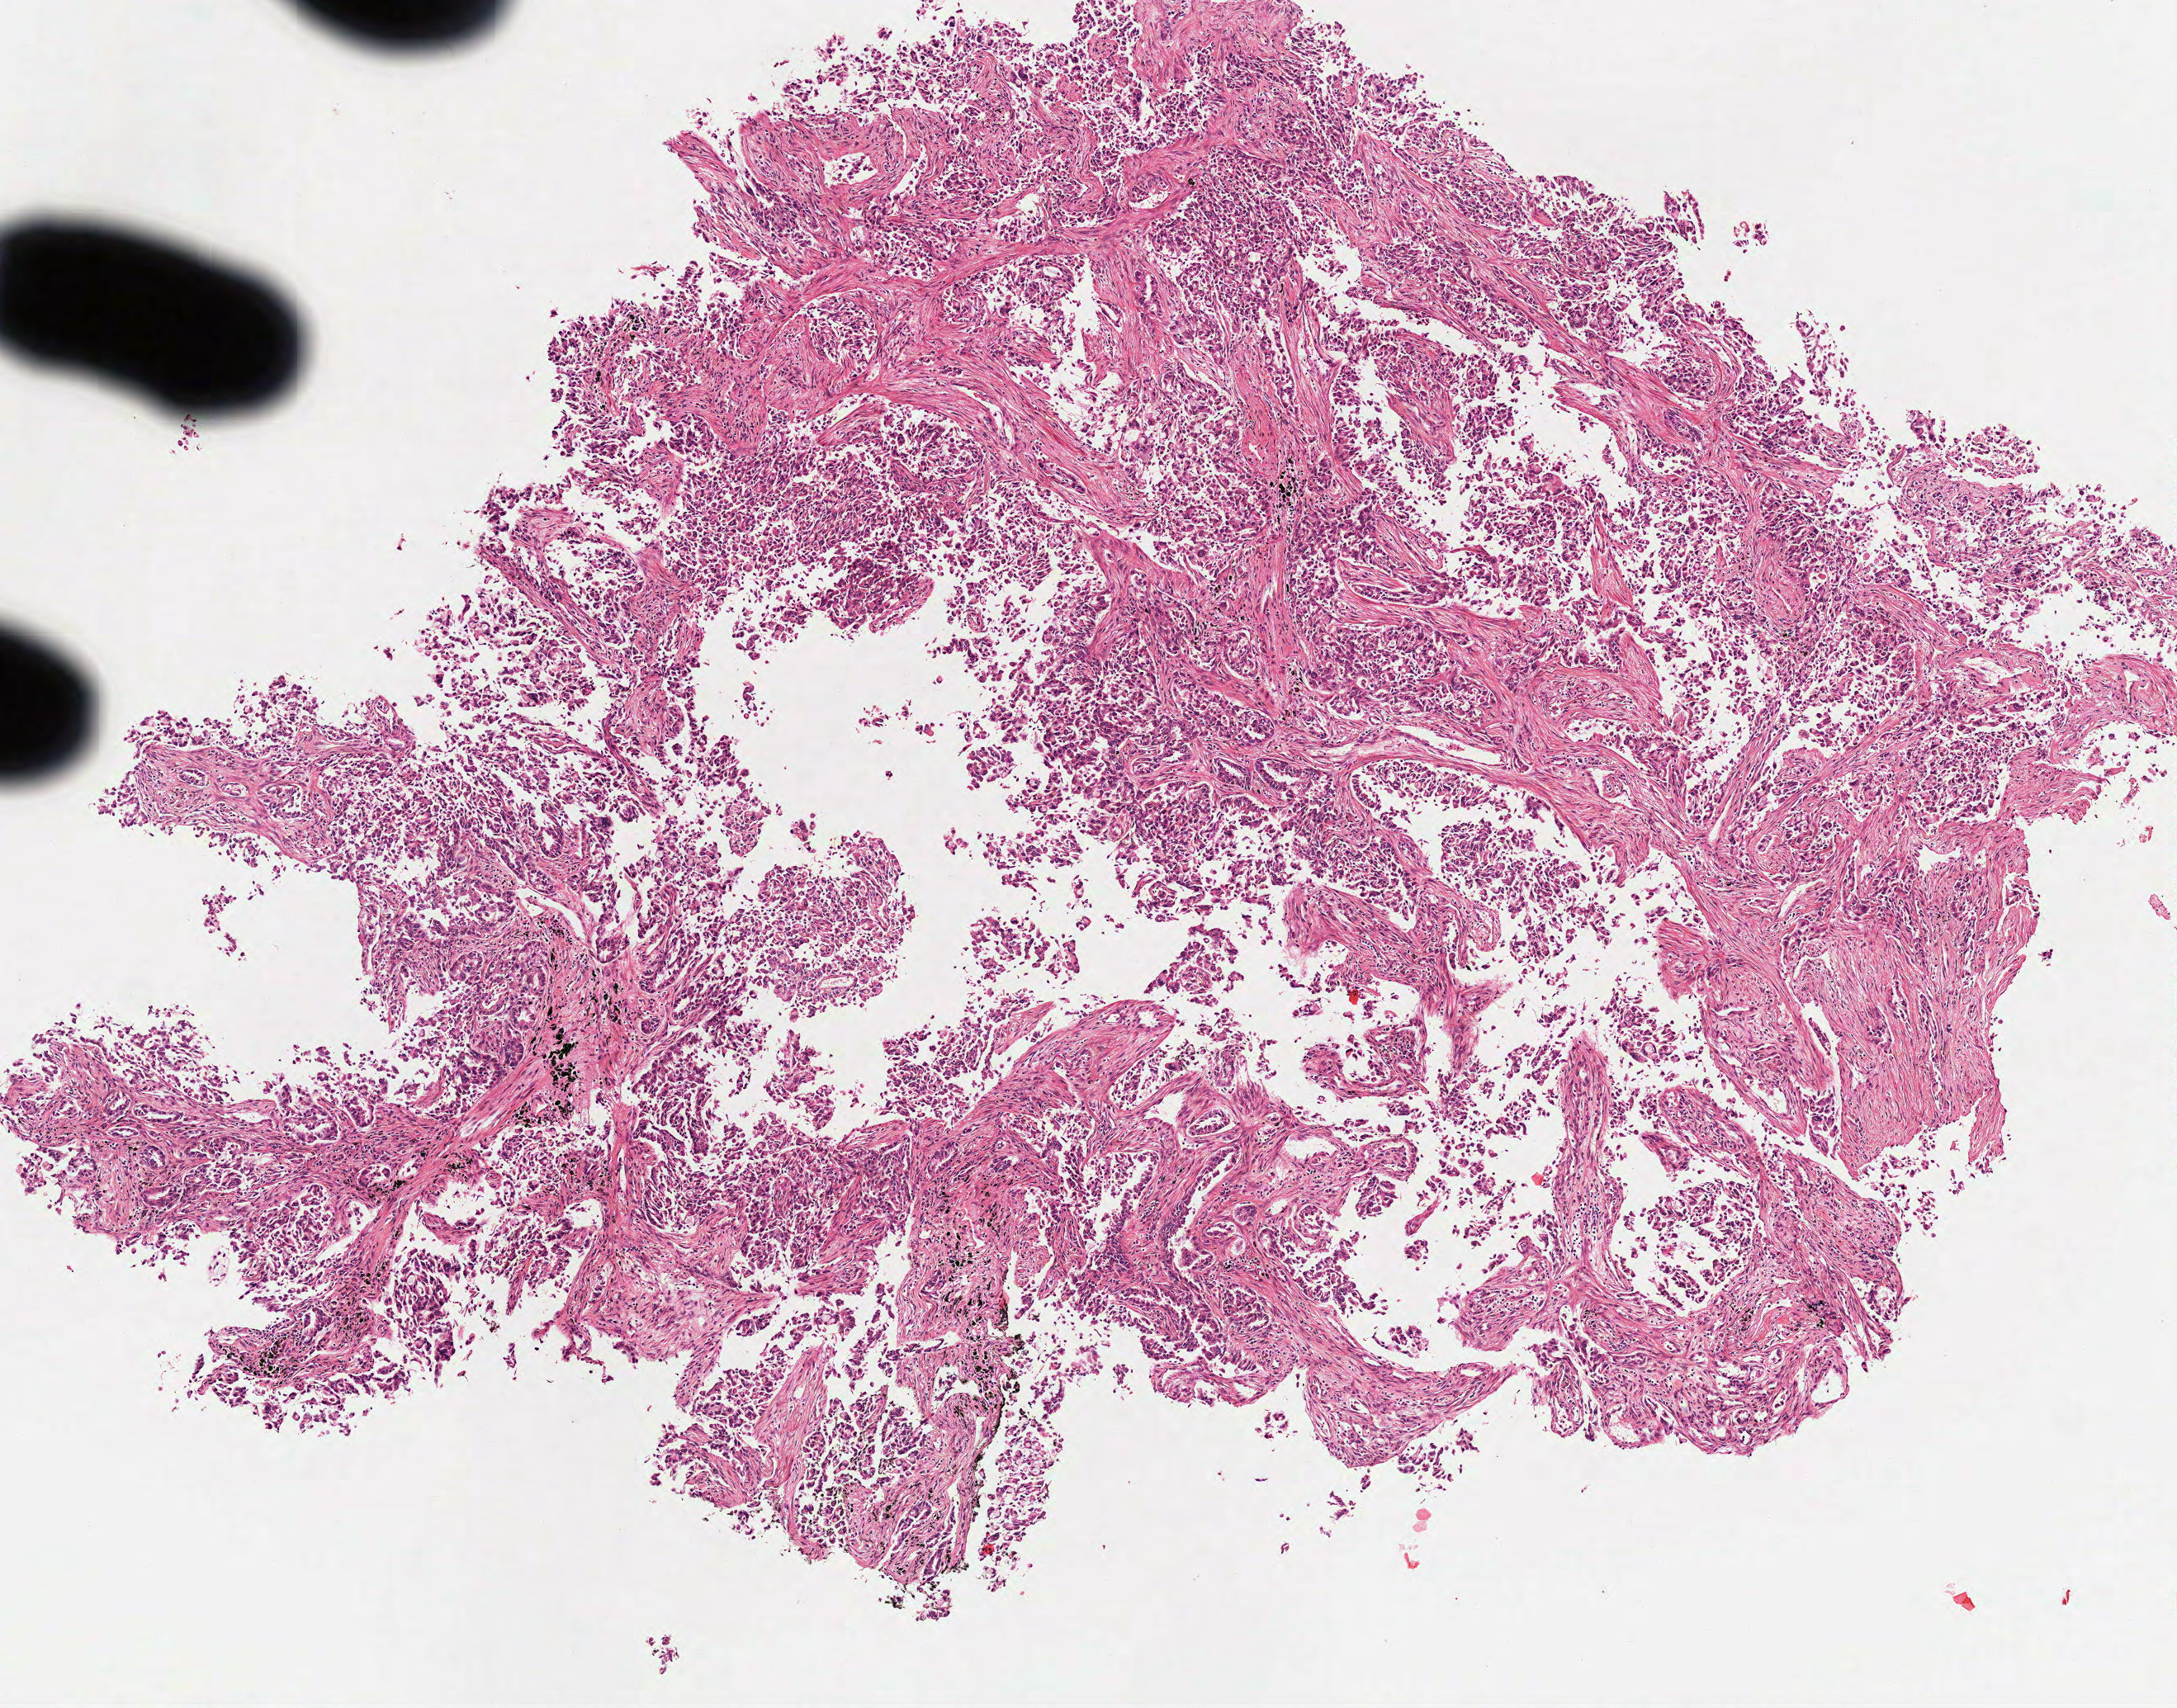
Digitized Hematoxylin and eosin (H&E) stained tissue section (whole slide) — low-resolution overview of the scanned area, about 5.3 x 4.2 mm (from a 40x scan); frozen section; primary tumour sample from the lung. Male, age 45 years at initial diagnosis.
Pathologic diagnosis: Adenocarcinoma, NOS (upper lobe, lung).